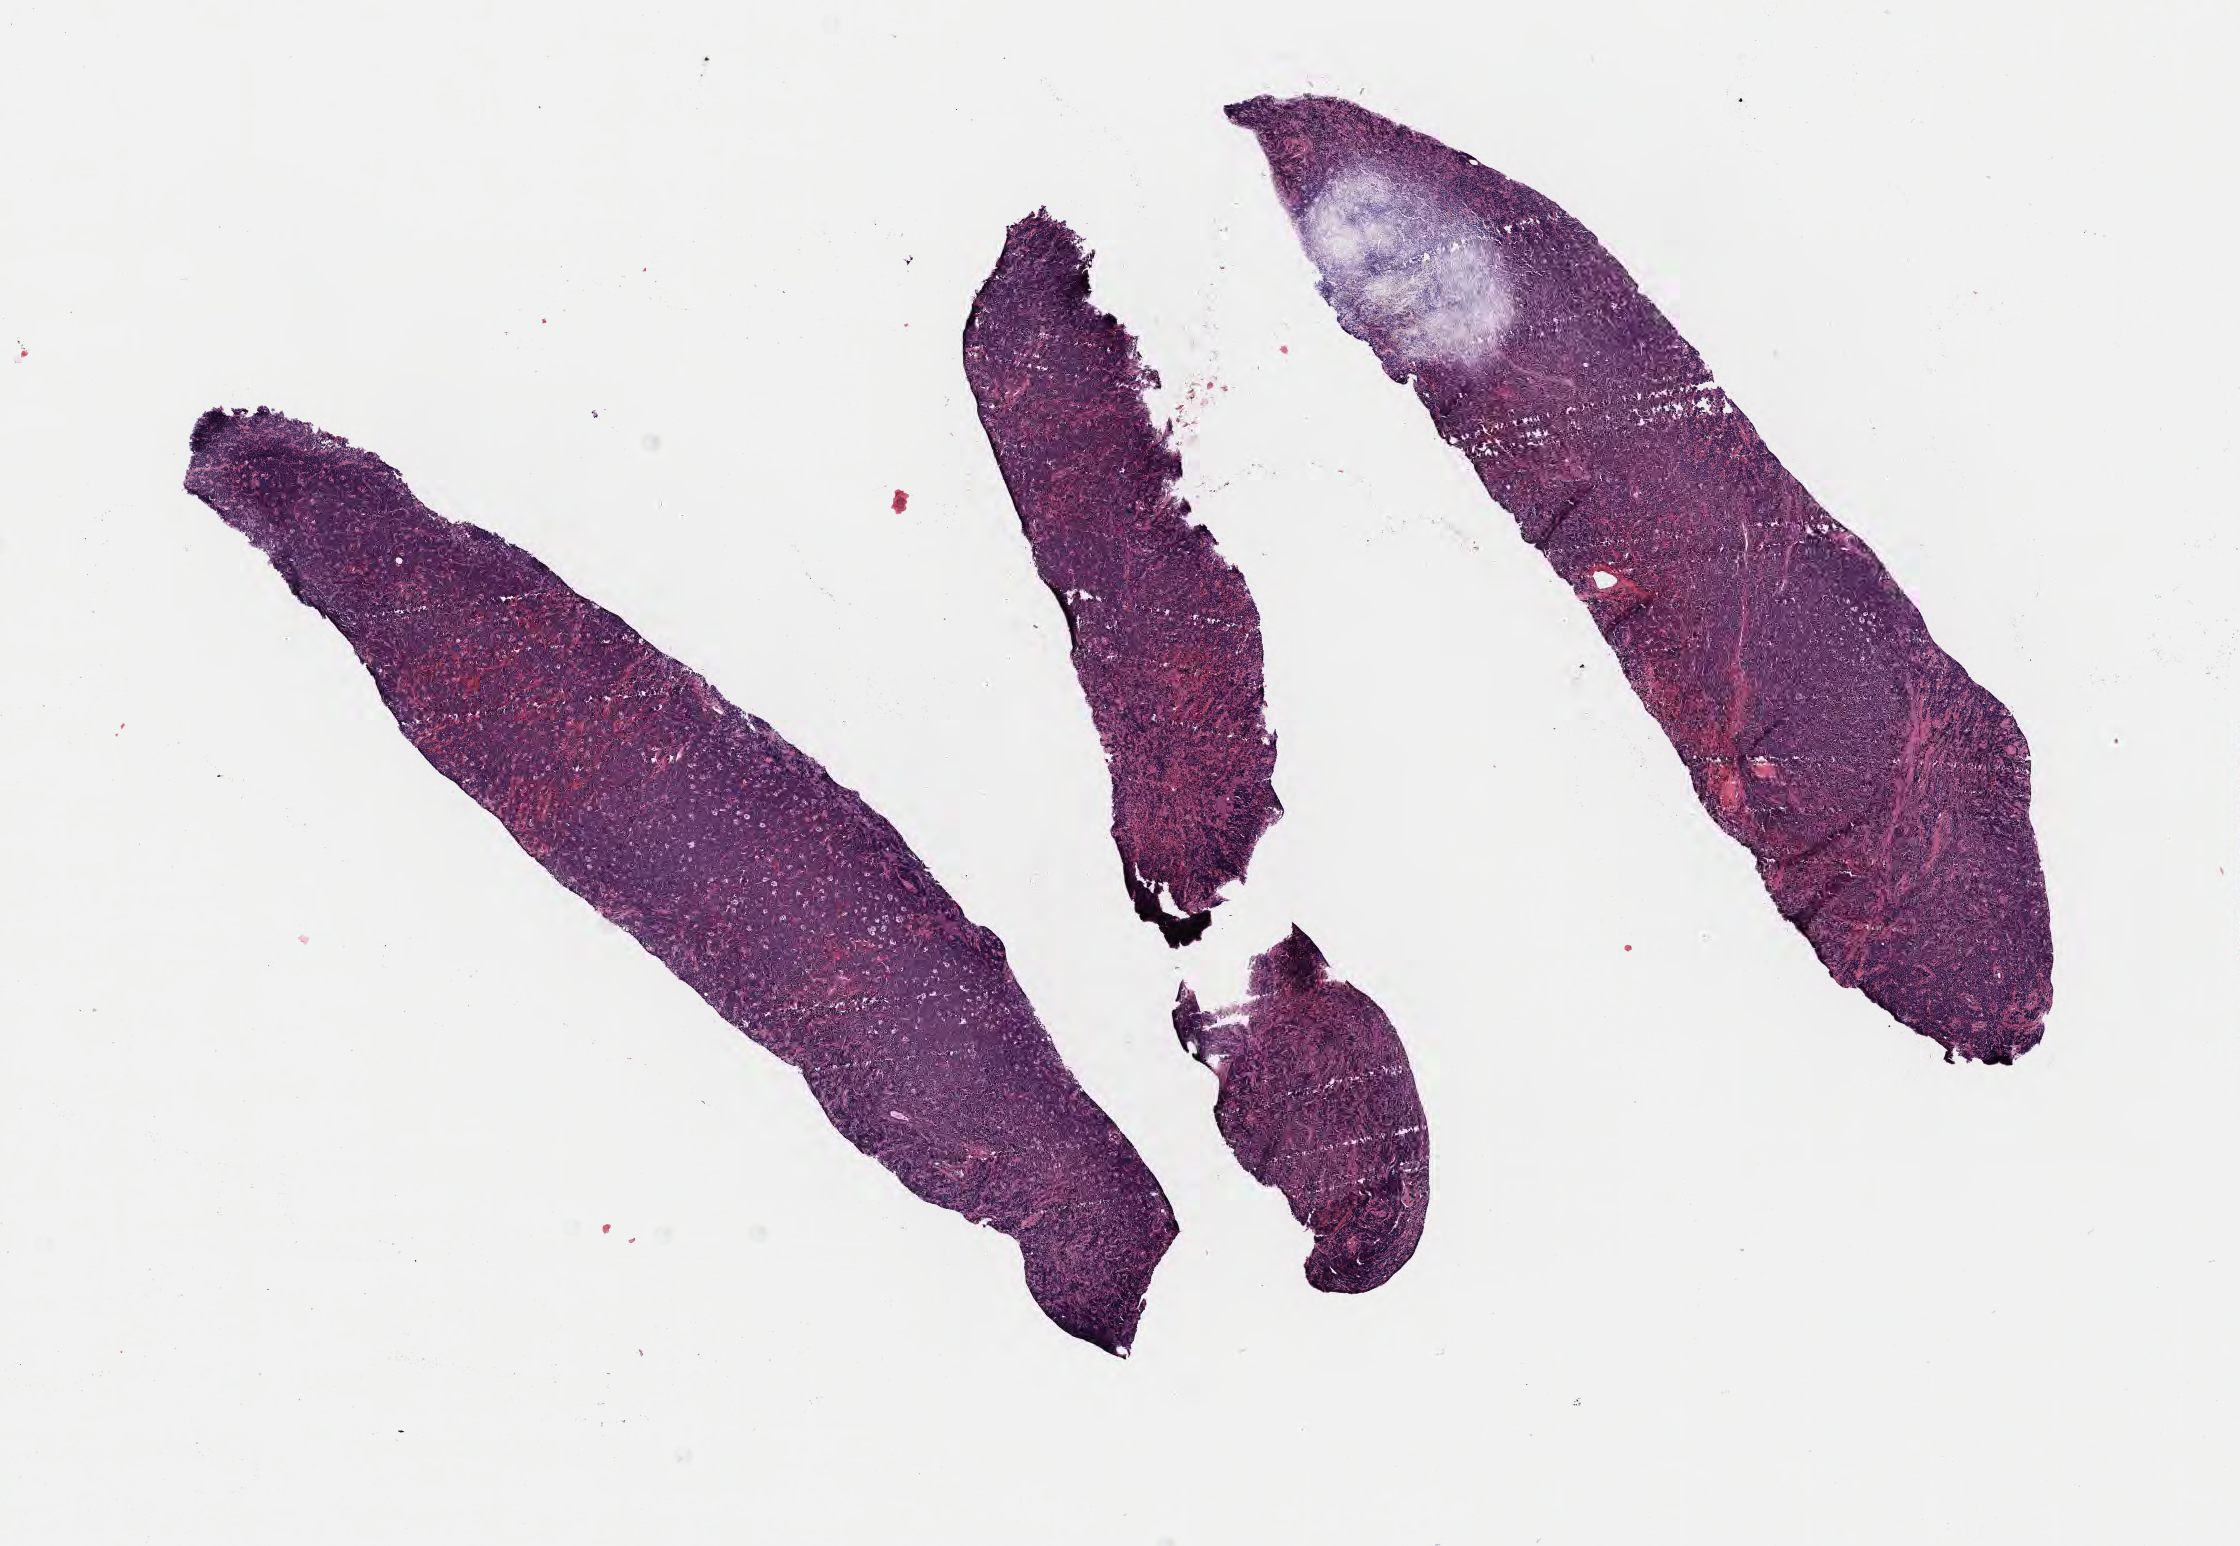
Whole-slide image, haematoxylin and eosin stain, low-resolution overview of the scanned area, about 9.1 x 6.3 mm. Specimen: tumor tissue. Female patient, aged 46.
- histologic diagnosis: Burkitt lymphoma, NOS